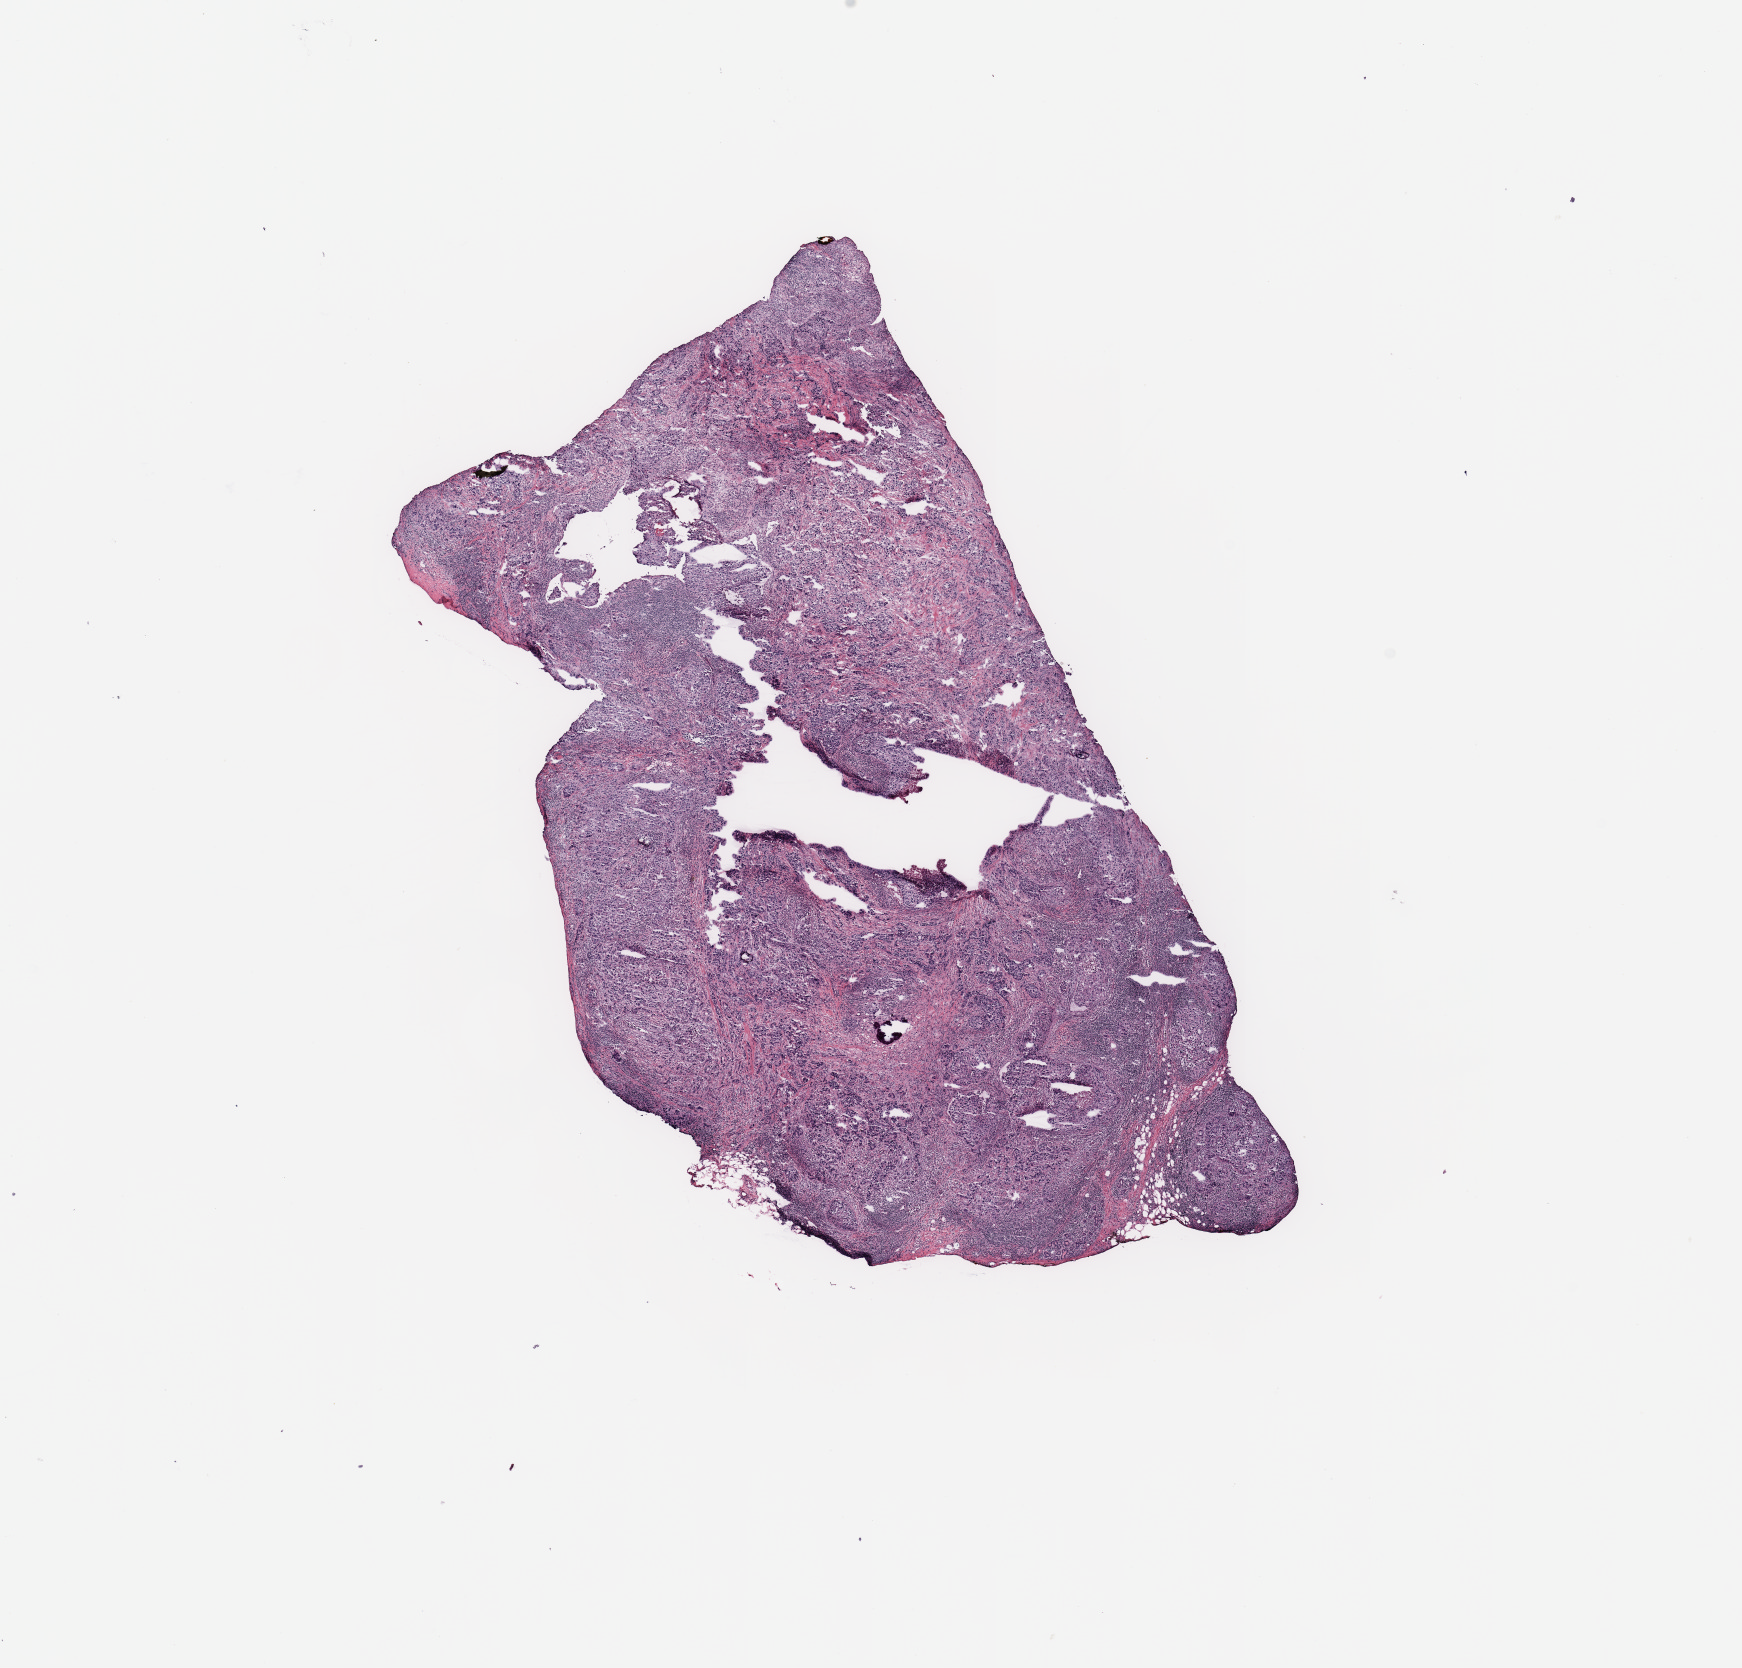
H&E whole-slide image — a low-resolution overview of the entire scanned area, about 13.8 x 13.2 mm (slide scanned at 20x); breast, tissue type not recorded.
Patient diagnosis (cohort enrolment): breast cancer (breast).